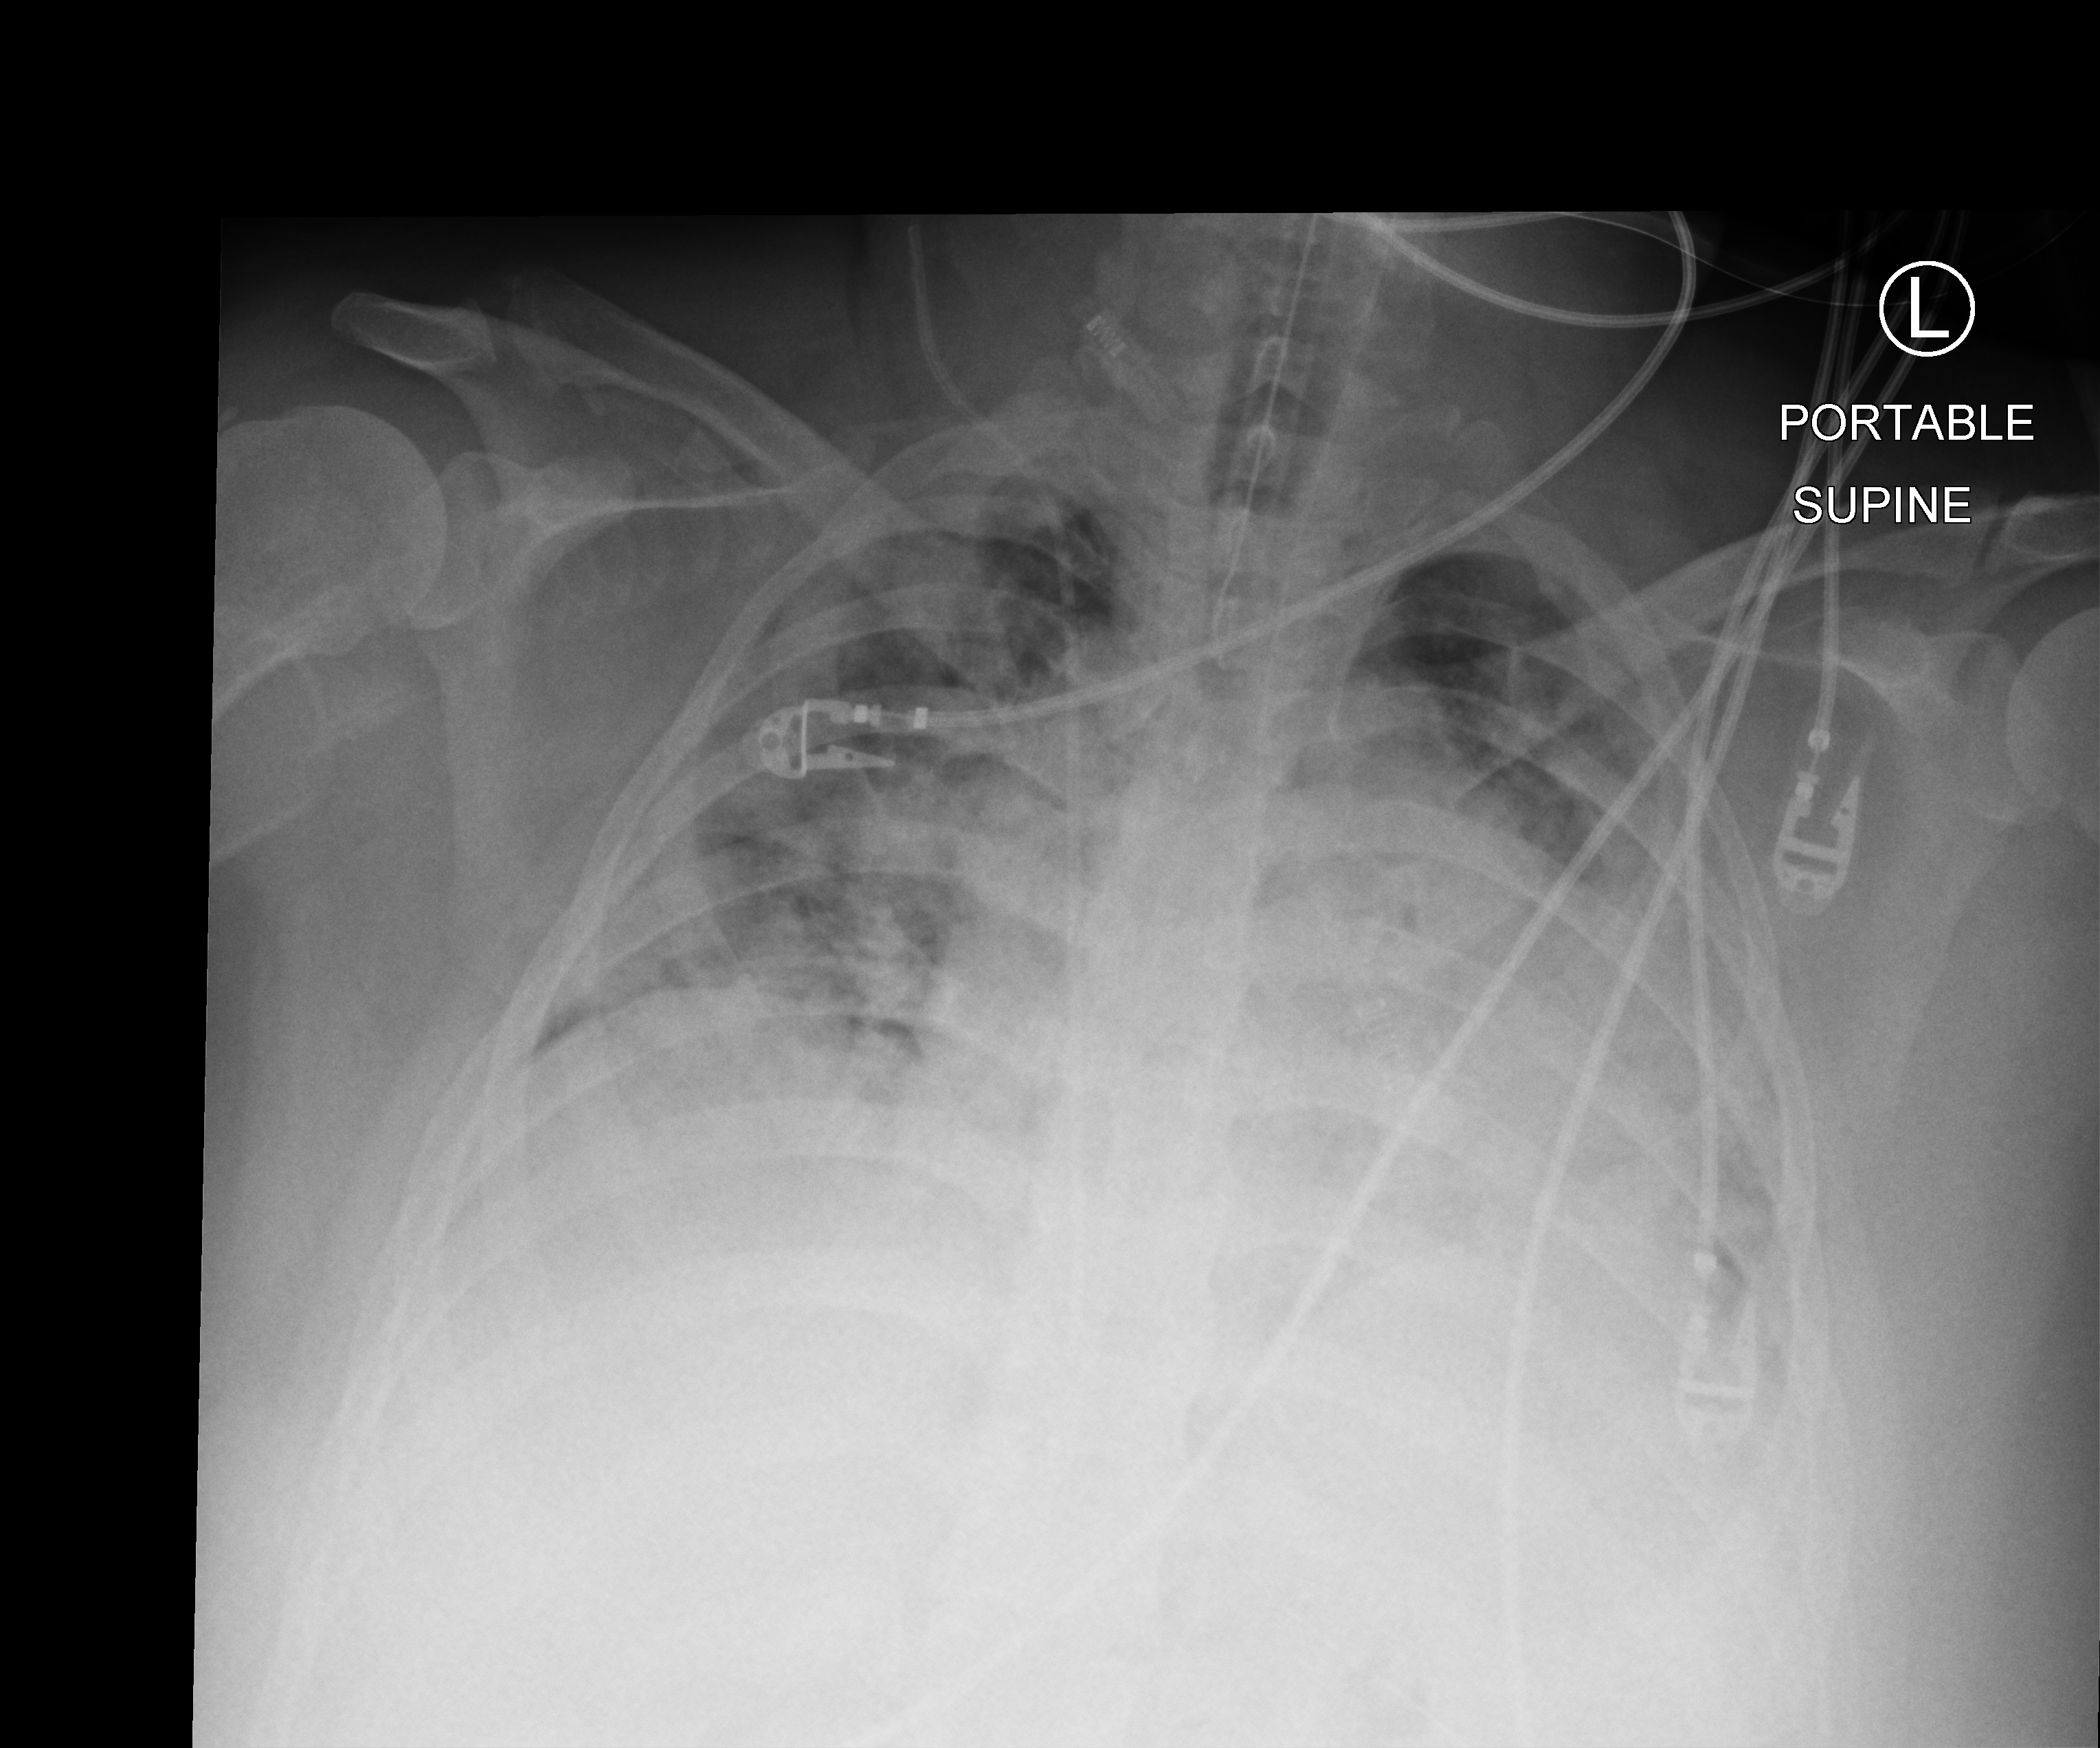
Portable chest radiograph, anteroposterior (AP) projection. Female patient hospitalised with COVID-19, age 18–59 years.
Admission-level facts for this patient (not findings on this image; timing relative to this image not recorded): admitted to intensive care during this hospital stay: yes; length of hospital stay: 25 days; mechanically ventilated during this hospital stay: yes.